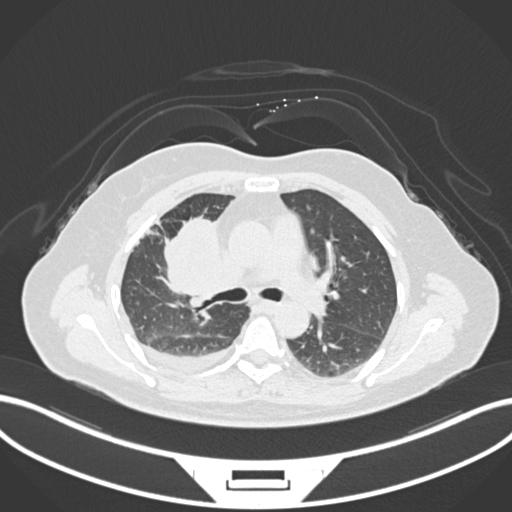
Chest CT, one axial slice; slice 92 of 172 in the series (ordered by position); reconstruction kernel B30f; 120 kVp; lung window (W 1500 / L -600 HU); 1 mm slice thickness; 512 × 512 image matrix. Patient: female, 52 years. From the clinical record (not read from this slice): clinical TNM (as recorded): T3 N1 M1.
Structures marked on this image (rectangle marked by the reading radiologist):
- lung tumour (recorded histology: adenocarcinoma): bounding box [x1, y1, x2, y2] px = [161, 213, 223, 306]